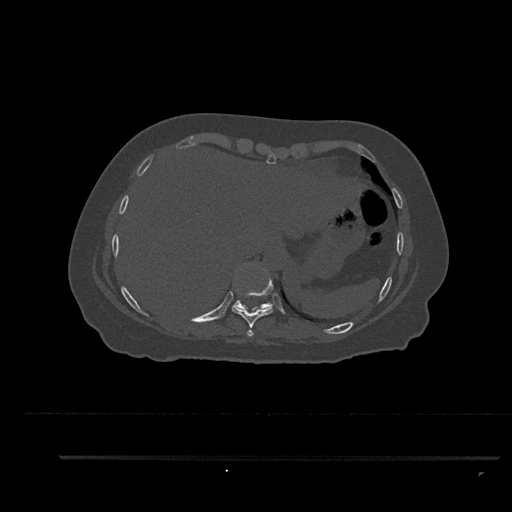
CT including the spine, one axial slice. Position 399 of 797 along the scan axis. Reconstruction kernel Br40s/3. 120 kVp. Bone window (W 1800 / L 400 HU). 512 × 512 image matrix, field of view 408 × 408 mm. Patient: female, 44 years. From the clinical record (not read from this slice): primary cancer: renal.
Outlined on this slice (semi-automatically segmented with operator editing):
- T10 vertebra: bounding box [x1, y1, x2, y2] px = [232, 300, 273, 310]
- T8 vertebra: [247, 329, 254, 337]
- T9 vertebra: [232, 266, 273, 328]